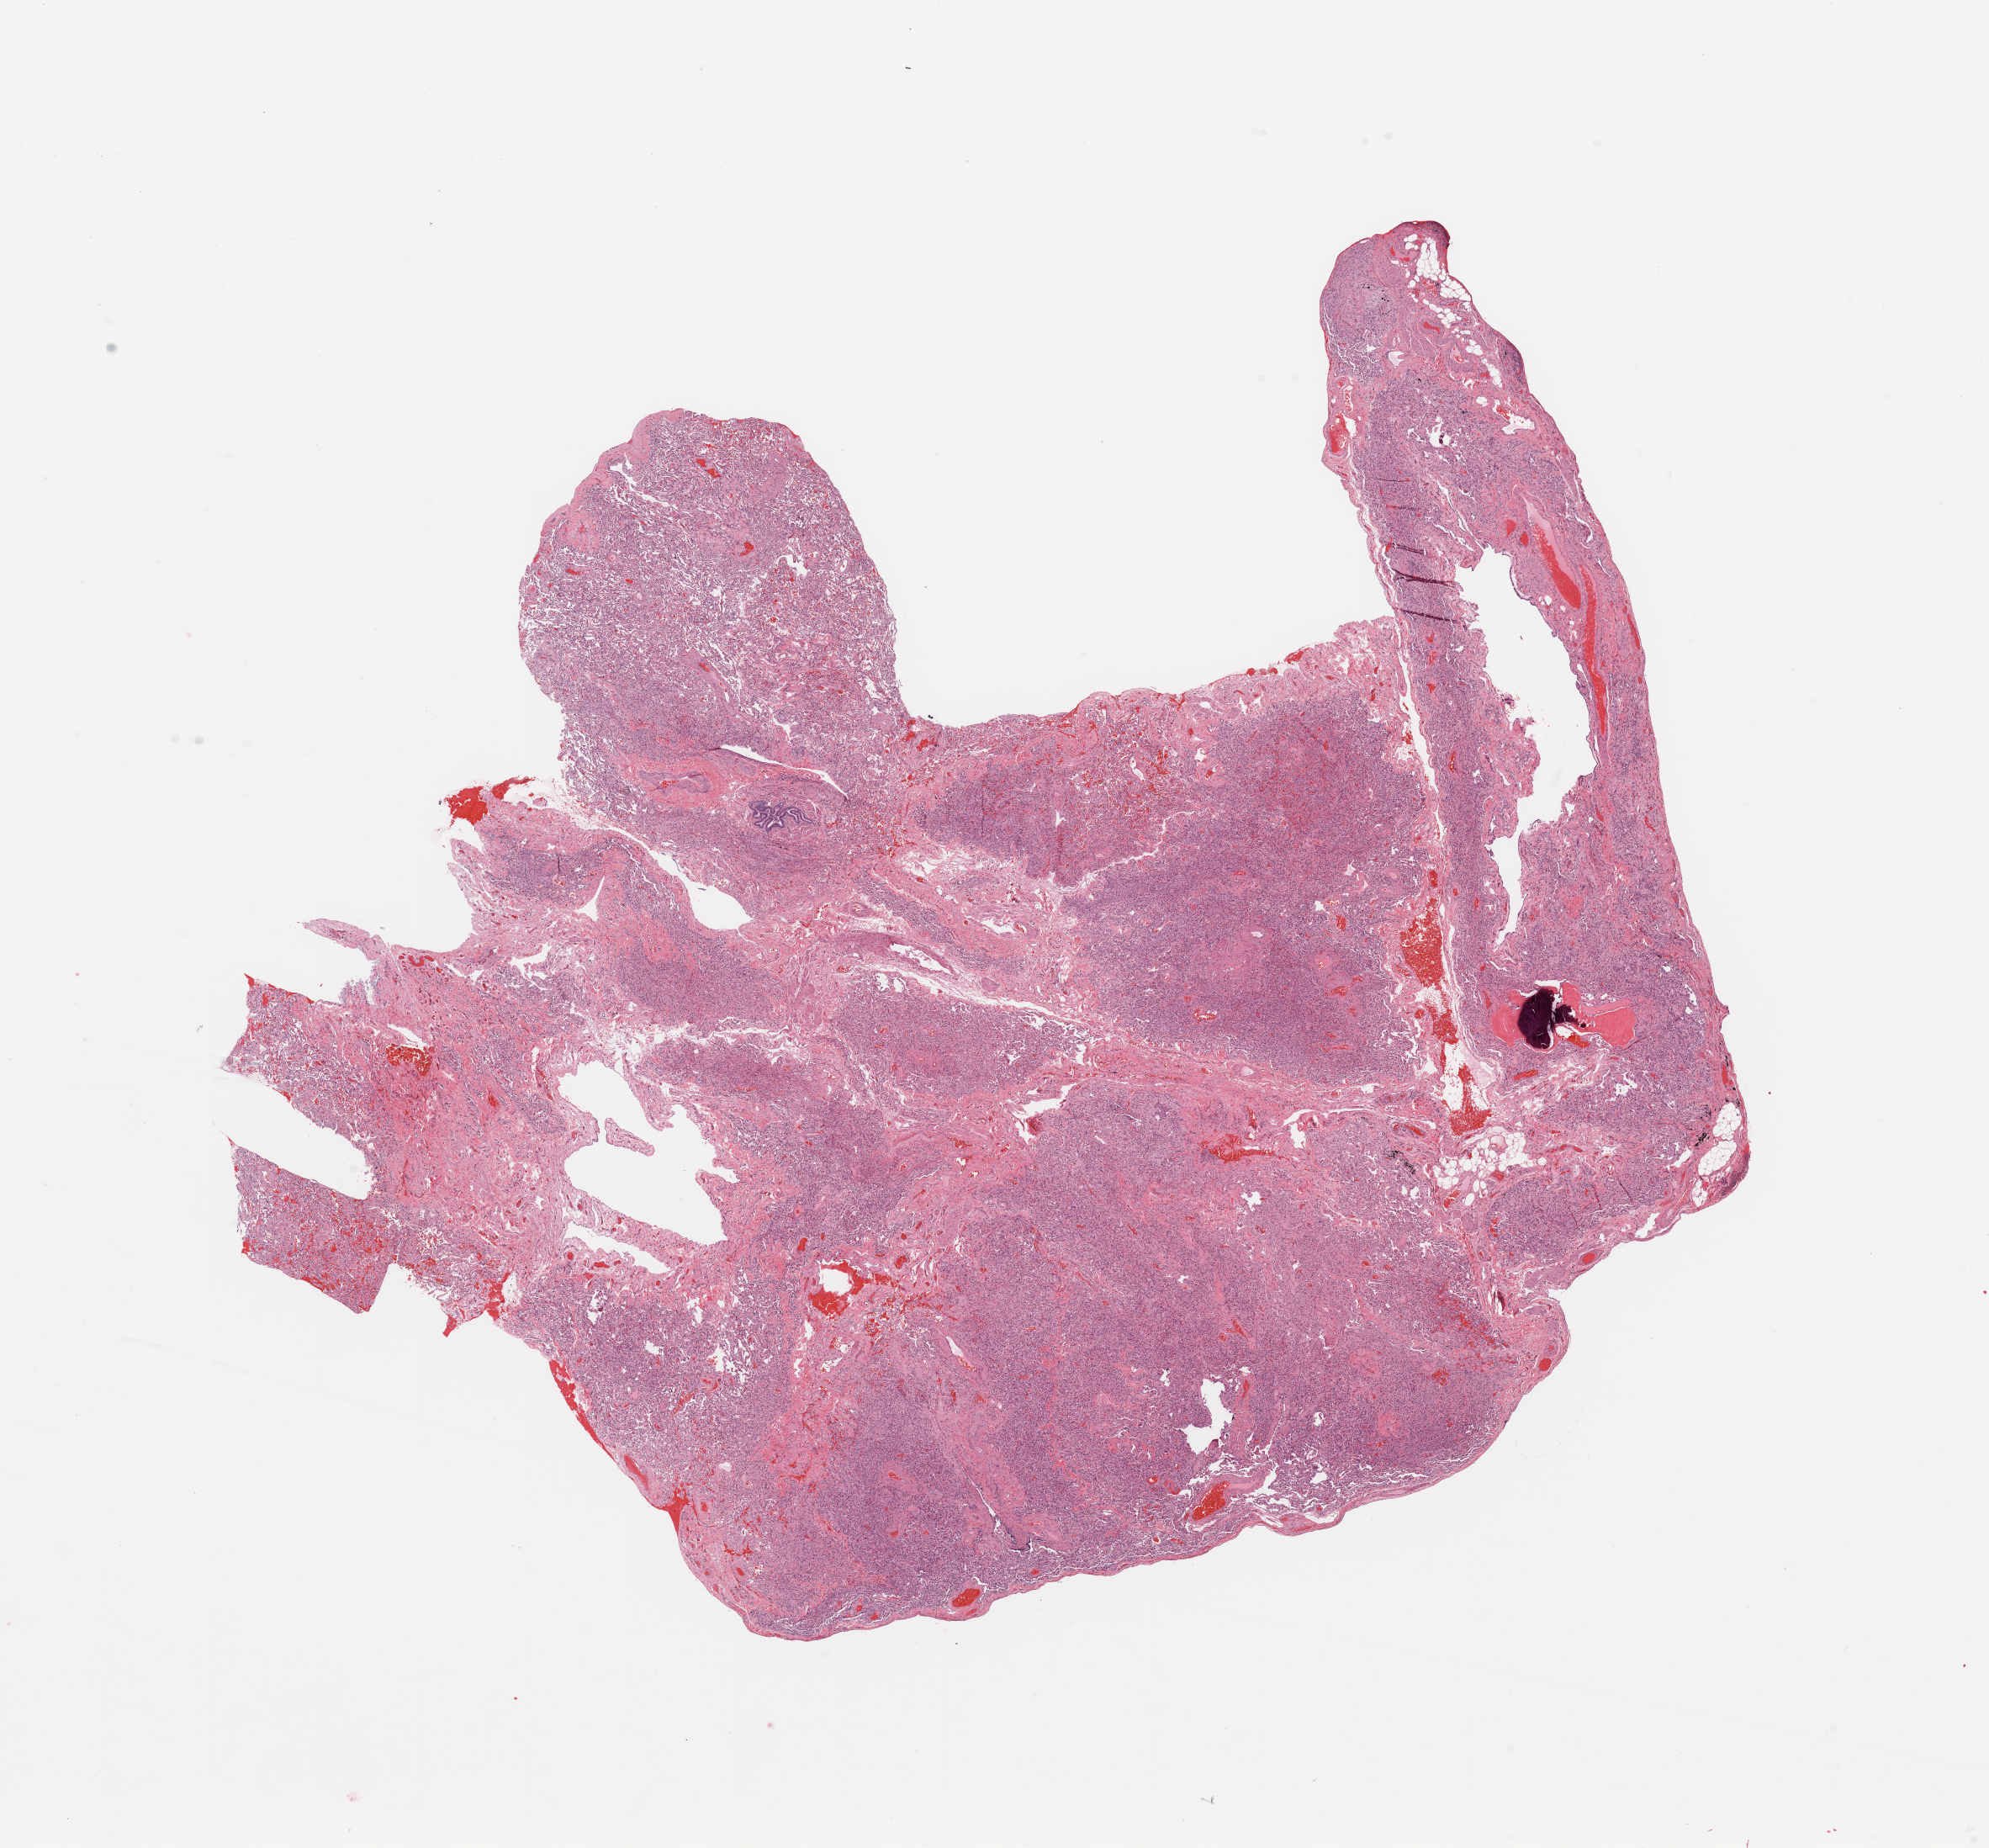
H&E-stained whole-slide image — shown as a low-resolution overview of the whole scanned area (about 18.7 x 17.4 mm, slide scanned at 20x), normal (non-tumour) tissue sample, sampled site: lung. Male, 77 y/o.
- this section: normal (non-tumour) tissue from the same patient
- patient diagnosis: Adenocarcinoma, NOS